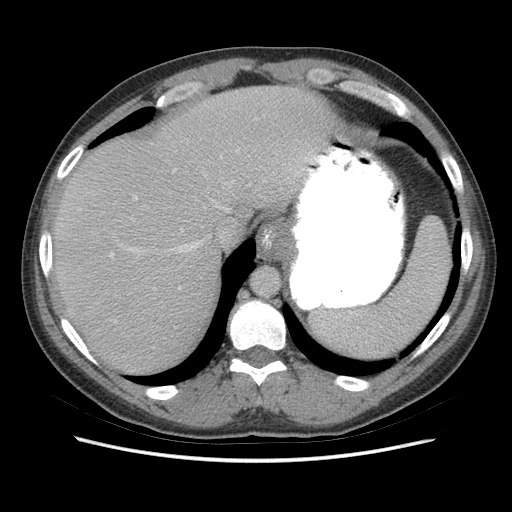
Contrast-enhanced abdominal CT (liver protocol), one axial slice. Slice 56 of 73 in the series (ordered by position). Reconstruction kernel STANDARD. 140 kVp. Soft-tissue window (W 400 / L 40 HU). 2.5 mm slice thickness. 512 × 512 image matrix. From the clinical record (not read from this slice): diagnosis: hepatocellular carcinoma (patient treated with transarterial chemoembolisation; whether this scan precedes or follows treatment is not stated here); TNM stage (as recorded): Stage-IIIA; Child-Pugh class: A; tumour size: 6.6 cm.
Structures marked on this image (semi-automatic segmentation, software-assisted and operator-edited):
- liver parenchyma outside the tumour (the mass and vessels are separate outlines, so this box may not span the whole liver): box from (x=52, y=86) to (x=334, y=374) px
- liver vessels: (x=110, y=155)–(x=317, y=289)